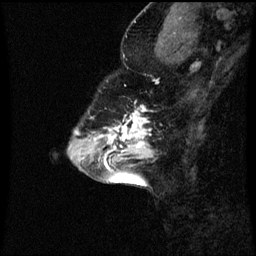
Breast MRI (dynamic contrast-enhanced), one sagittal slice. Slice 22 of 60 in the series (ordered by position). Dynamic contrast-enhanced series, image 2 of 3 at this slice position (ordered by acquisition). 1.5 T. TE 4.2 ms, TR 8.9 ms. 2 mm slice thickness. 256 × 256 image matrix. Female patient, age 43 years. From the clinical record (not read from this slice): setting: breast cancer imaged before/during neoadjuvant chemotherapy; receptor status: HR-positive, HER2-negative.
Annotated regions visible in this slice (semi-automatic segmentation, software-assisted and operator-edited):
- analysis volume of interest (the breast-tissue region the enhancement analysis was run in; not a lesion): box from (x=96, y=108) to (x=155, y=159) px
- tumour enhancement mask (voxels above the 70 % enhancement threshold inside the analysis volume of interest): (x=104, y=108)–(x=151, y=159)